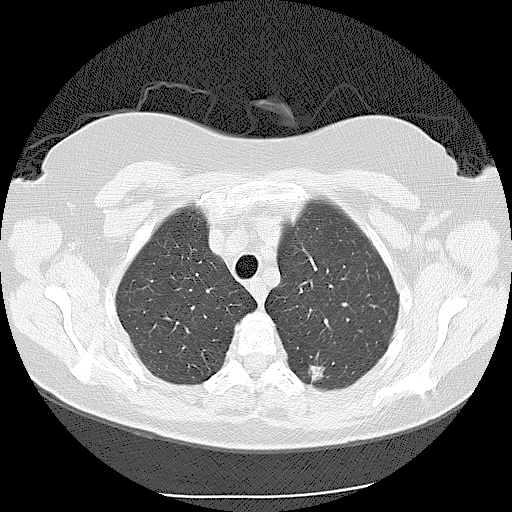
Axial slice from a low-dose chest CT screening exam; second screening round (one year after baseline); lung window (W 1500 / L -600 HU); 120 kVp; 512 × 512 image matrix, field of view 360 × 360 mm. Female participant, aged 56 years at enrolment.
Expert-annotated lung lesion, box from (x=290, y=346) to (x=345, y=396) px. The exam's reader record, not a measurement of the box and not confirmed to be the same lesion: non-calcified nodule or mass ≥4 mm, left lower lobe, 9 × 9 mm, spiculated (stellate) margins, soft tissue attenuation, pre-existing on the prior screen: yes; interval growth: yes. Later outcome: lung cancer diagnosed 173 days after this screen — adenocarcinoma, NOS, left lower lobe, moderately differentiated (G2), stage IIA (AJCC 6th edition), 15 mm at pathology.